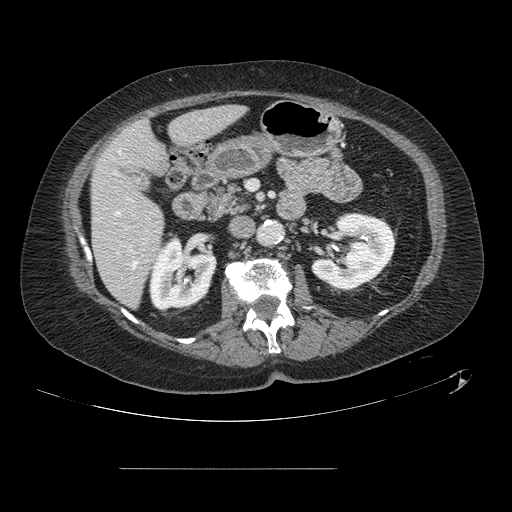
Contrast-enhanced abdominal CT, one axial slice. Slice 49 of 148 in the series (ordered by position). 120 kVp. Soft-tissue window (W 400 / L 40 HU). 512 × 512 image matrix, field of view 439 × 439 mm. Female patient, age 75 years. From the clinical record (not read from this slice): diagnosis: colorectal cancer liver metastases, imaged before liver resection; multiple liver metastases: no; largest metastasis: 2.4 cm; disease in both lobes: no.
Annotated regions visible in this slice (expert manual segmentation):
- hepatic veins: box from (x=116, y=212) to (x=137, y=268) px
- liver: (x=92, y=106)–(x=242, y=306)
- planned liver remnant (the part of the liver to remain after resection): (x=92, y=106)–(x=243, y=306)